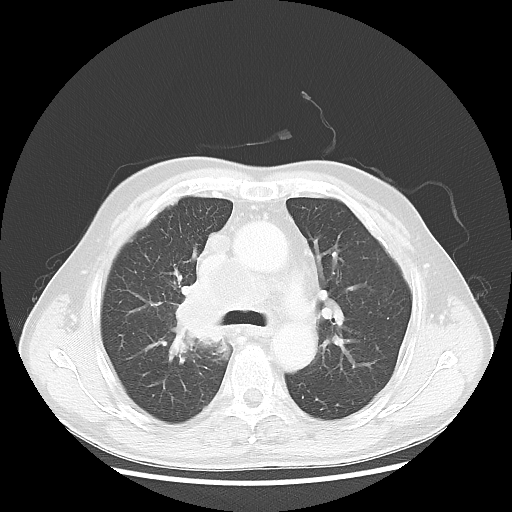
Chest CT, one axial slice; slice 37 of 60 in the series (ordered by position); reconstruction kernel LUNG; lung window (W 1500 / L -600 HU); 512 × 512 image matrix. Male patient, age 64 years. Case-level facts recorded for this patient, not image findings: clinical TNM (as recorded): T3 N3 M0; histopathological grade: G3.
Outlined on this slice (rectangle marked by the reading radiologist):
- lung tumour (recorded histology: small cell carcinoma): bounding box (x1, y1, x2, y2) in pixels: (169, 286, 237, 351)